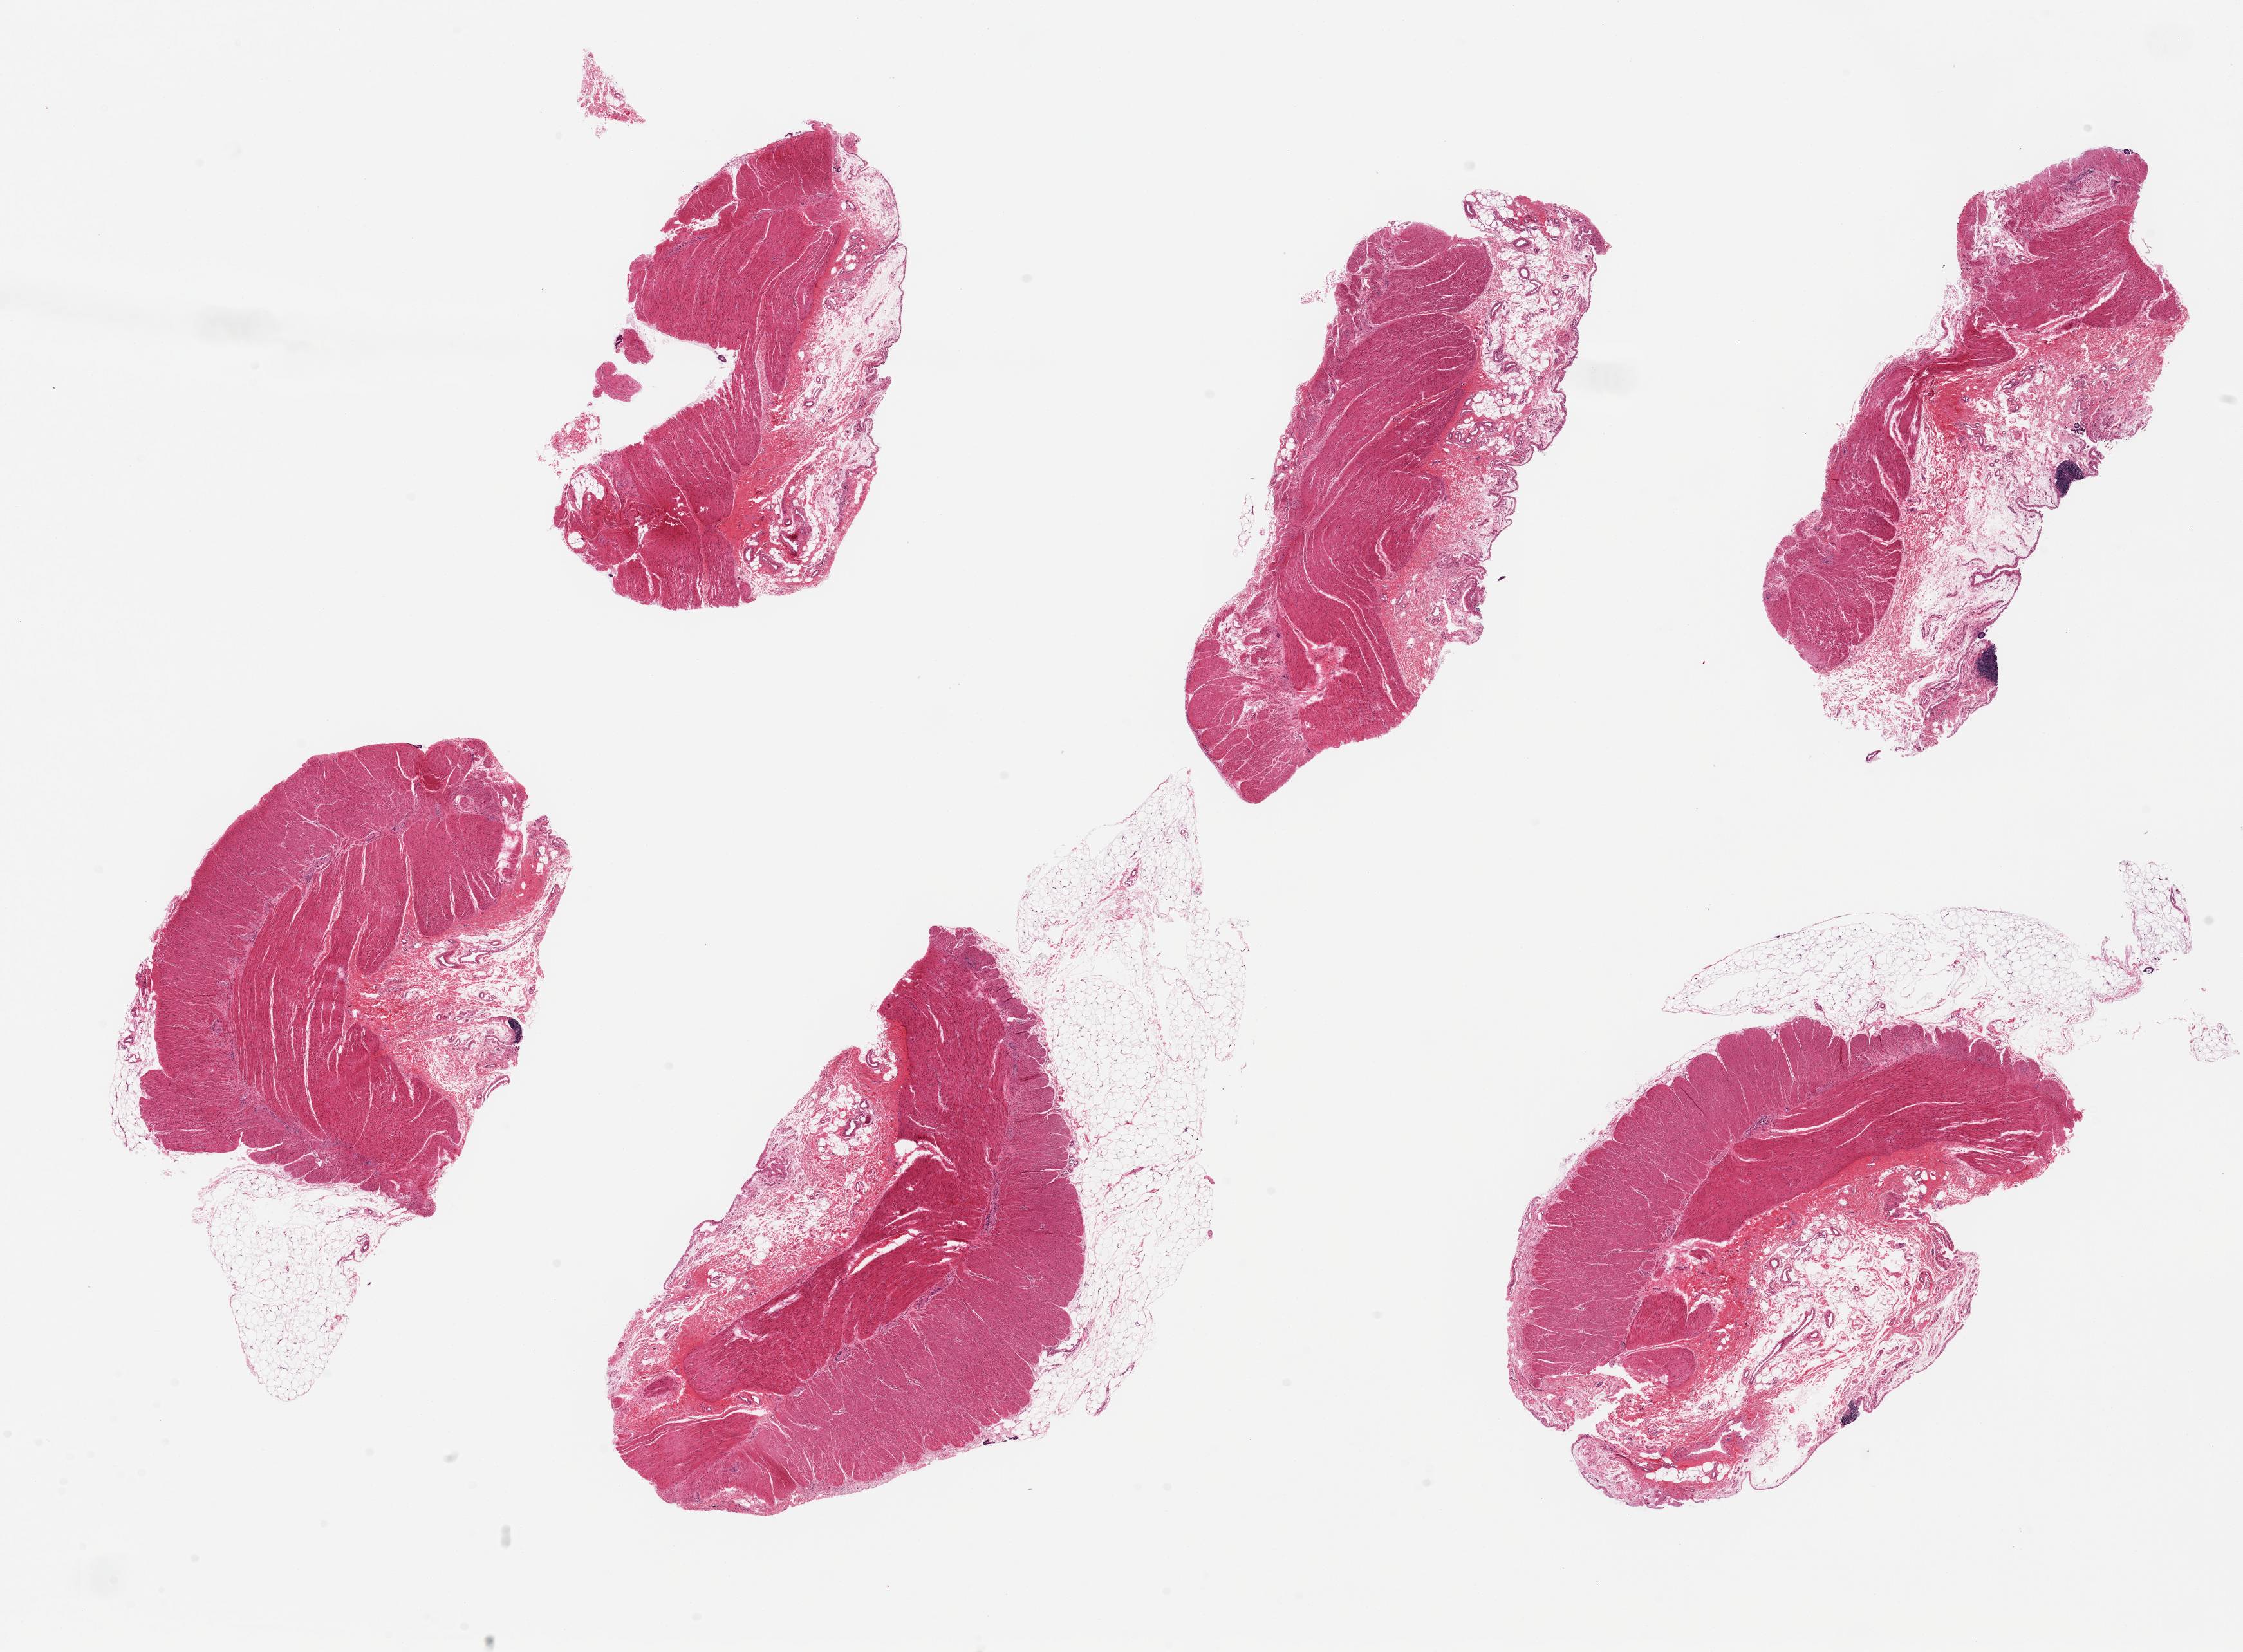
Whole-slide image, haematoxylin and eosin stain, brightfield, whole scanned area (about 27.6 x 20.3 mm) shown as a low-resolution overview; PAXgene-fixed, paraffin-embedded tissue; section of sigmoid colon (target tissue); donor tissue sample.
* pathologist's review note for this sample: 6 pieces, ~9x2mm. Muscularis and fat, presumed sigmoid aliquots 1525 below